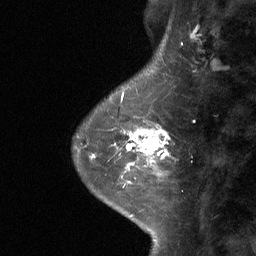
Breast MRI (dynamic contrast-enhanced), one sagittal slice. Slice 18 of 64 in the series (ordered by position). Dynamic contrast-enhanced study with each time point stored as its own series, time point 2 of 3 at this slice position (early post-contrast, ordered by acquisition time). 1.5 T. TE 4.8 ms, TR 27 ms. 2 mm slice thickness. 256 × 256 image matrix, field of view 180 × 180 mm. Patient: female, 42 years. Case-level facts recorded for this patient, not image findings: setting: breast cancer imaged before/during neoadjuvant chemotherapy; receptor status: triple-negative.
Annotated regions visible in this slice (semi-automatically segmented with operator editing):
- analysis volume of interest (the breast-tissue region the enhancement analysis was run in; not a lesion): bounding box (x1, y1, x2, y2) in pixels: (111, 104, 170, 178)
- tumour enhancement mask (voxels above the 90 % enhancement threshold inside the analysis volume of interest): (126, 128, 169, 174)